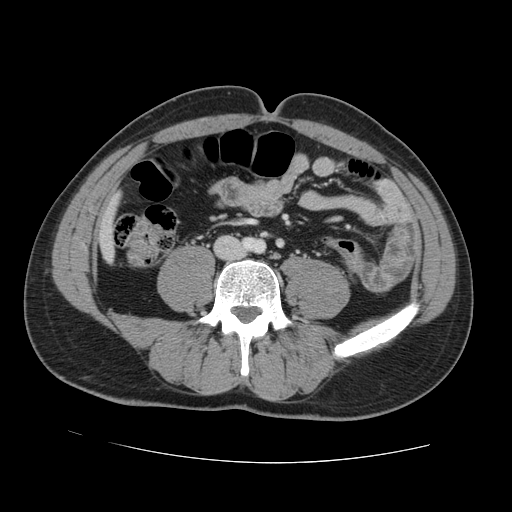
Contrast-enhanced abdominal CT, one axial slice; 120 kVp; soft-tissue window (W 400 / L 40 HU); 512 × 512 image matrix. Male patient, age 40 years. Case-level facts recorded for this patient, not image findings: diagnosis: colorectal cancer liver metastases, imaged before liver resection; multiple liver metastases: yes; largest metastasis: 2.9 cm; disease in both lobes: yes.
Structures marked on this image (expert manual segmentation):
- liver: bounding box [x1, y1, x2, y2] px = [101, 204, 116, 257]